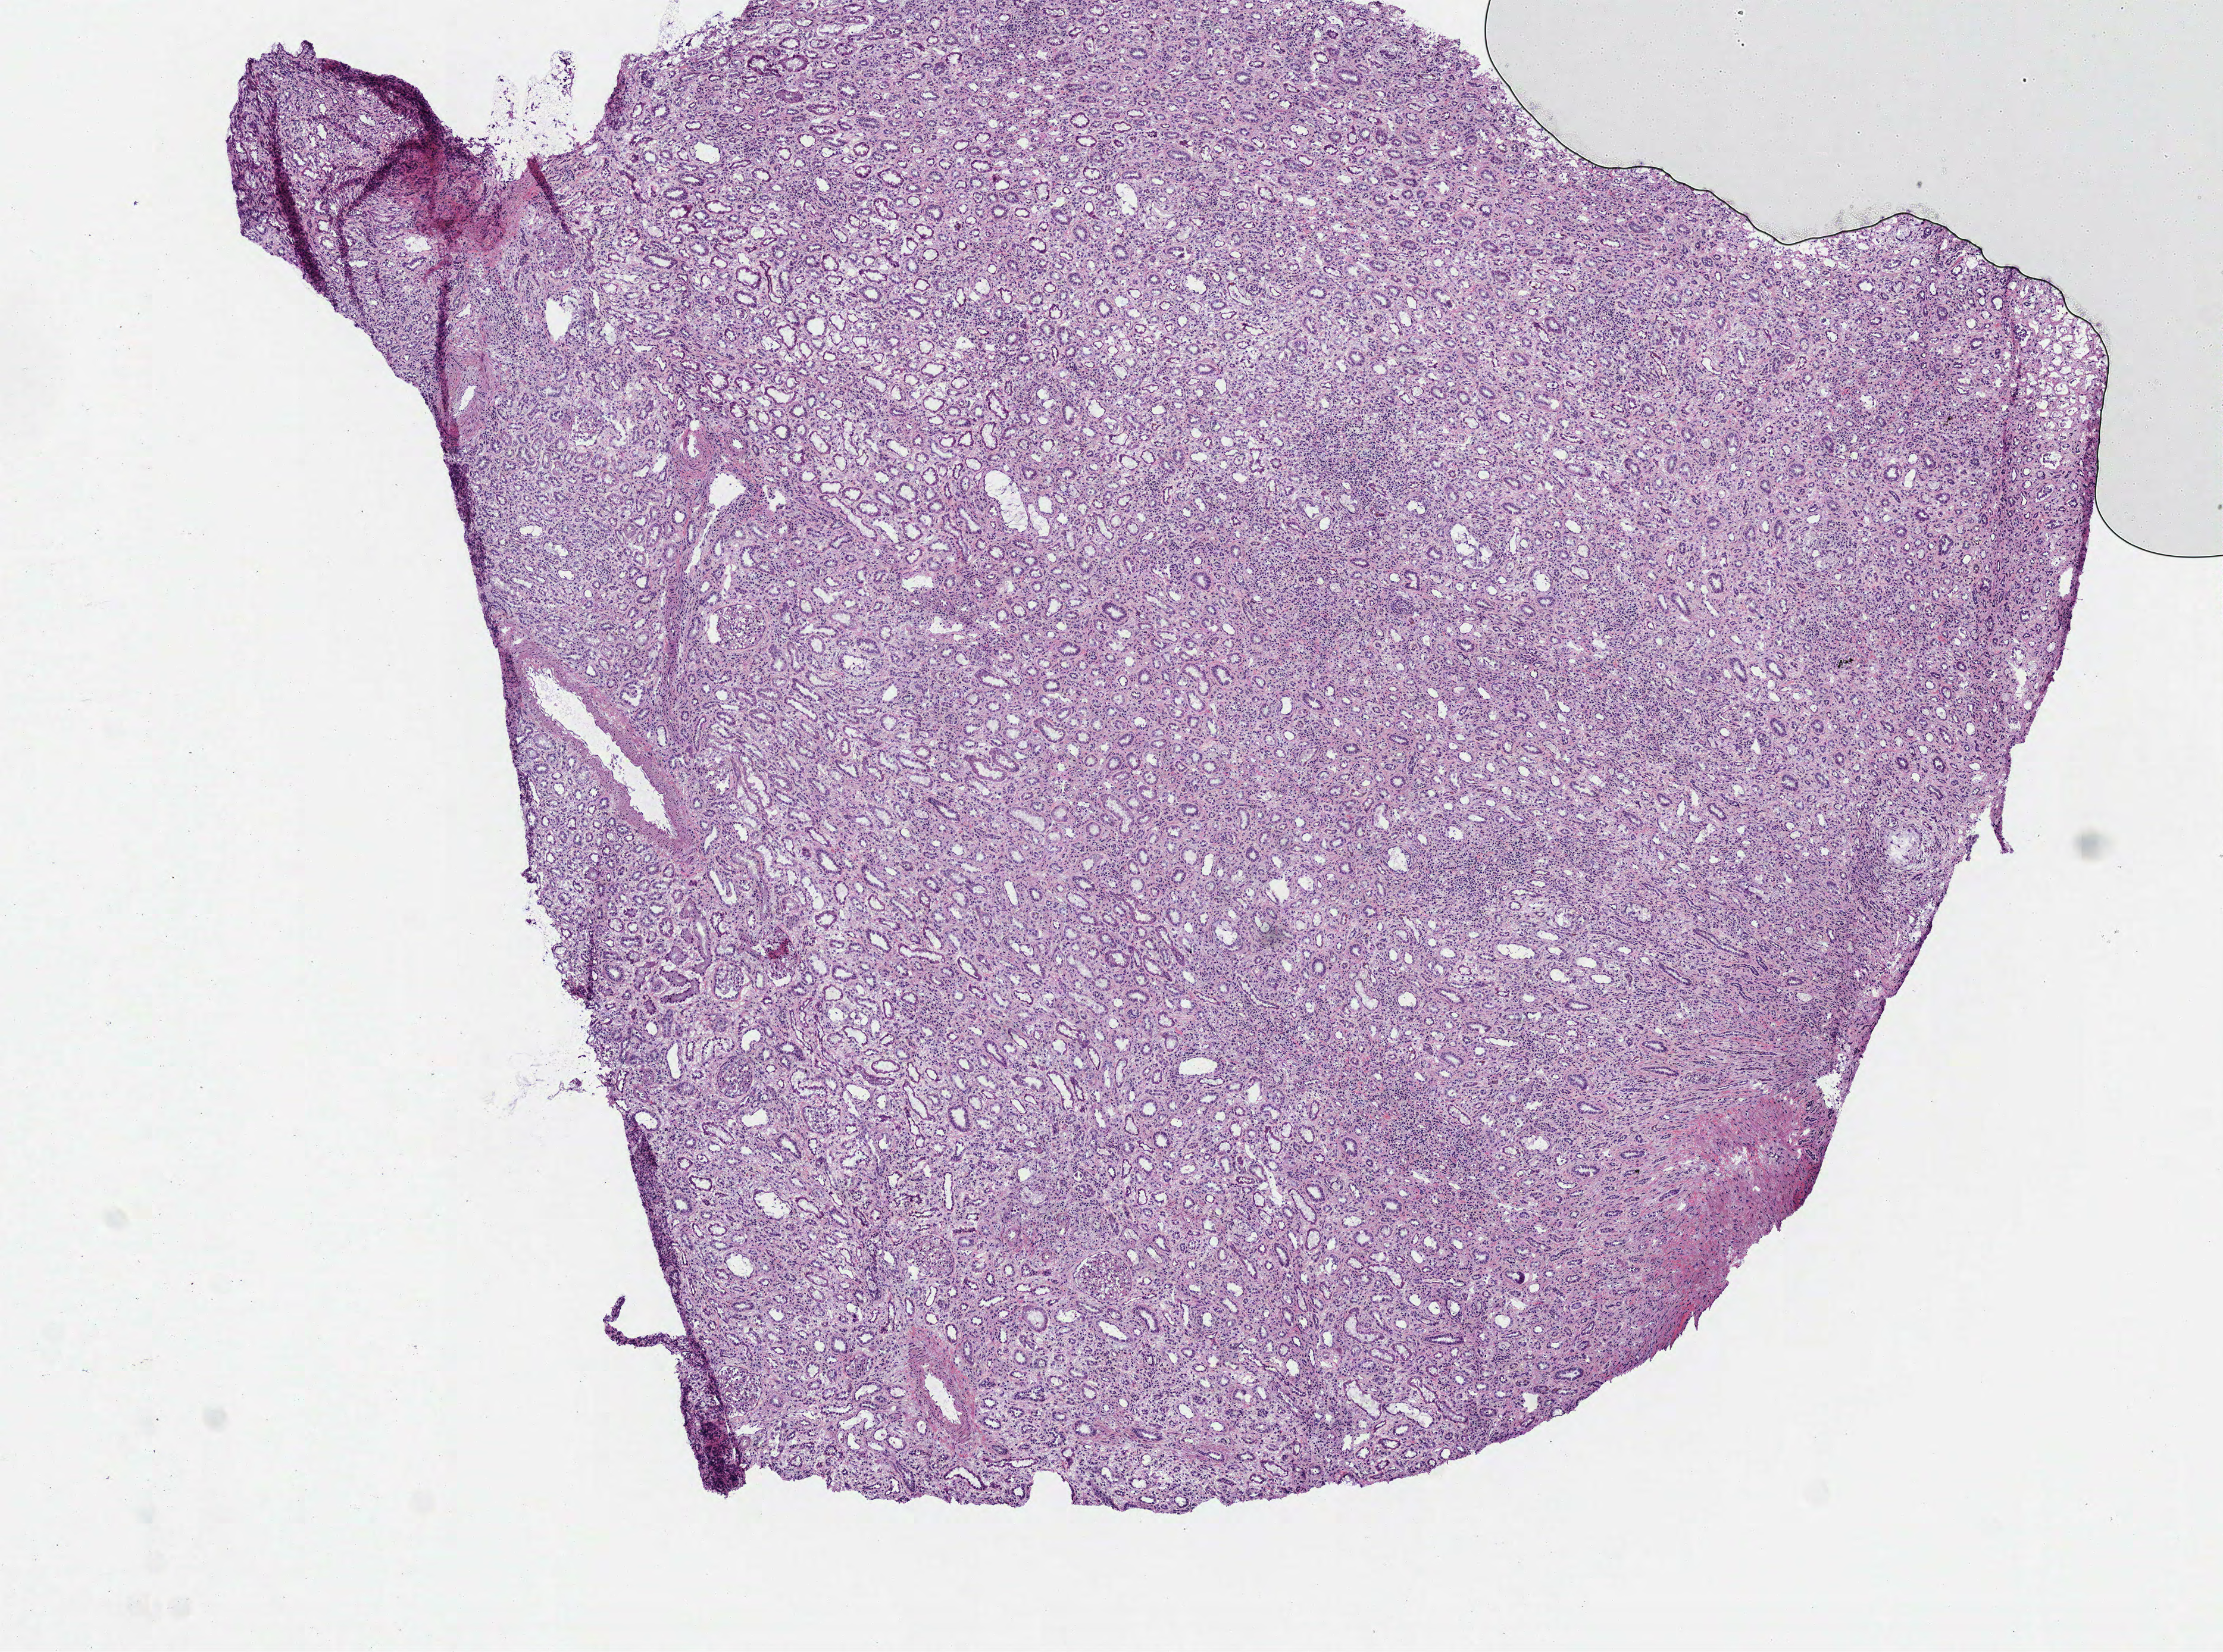
H&E-stained whole-slide image — low-resolution overview of the scanned area, about 7.5 x 5.6 mm. Frozen section. Solid tissue normal (non-tumour tissue) sample from the kidney. Female, age 28 years at initial diagnosis. Infiltration values recorded for this section: lymphocyte infiltration 5%, monocyte infiltration 0%, neutrophil infiltration 0%.
• this section: solid tissue normal (non-tumour) sample from the same patient
• patient diagnosis: Papillary adenocarcinoma, NOS